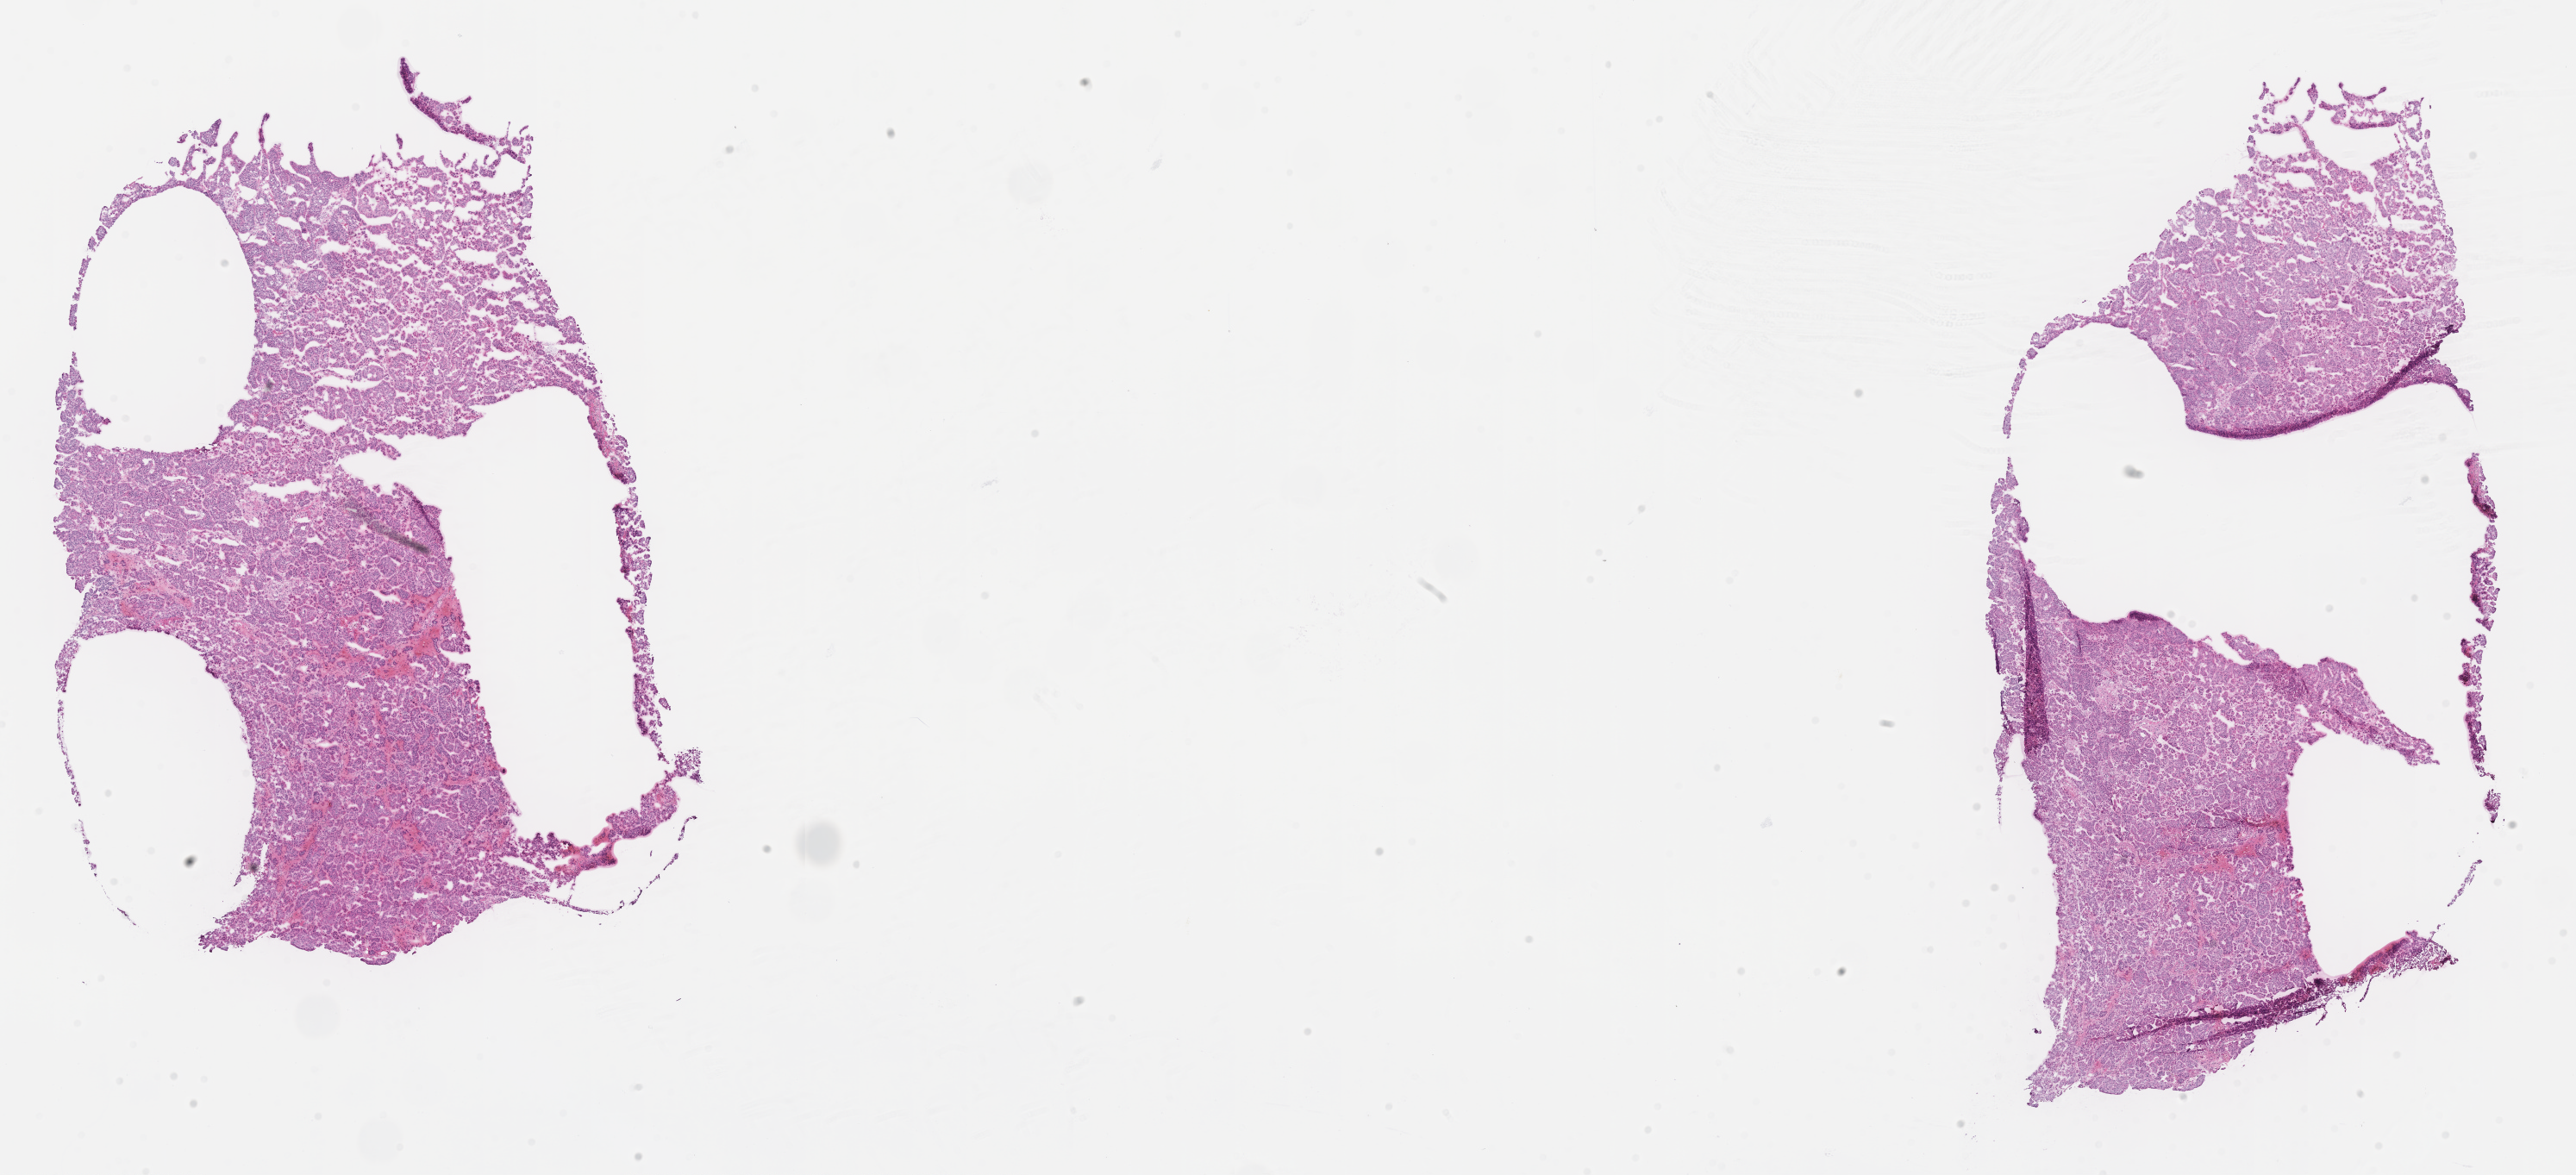
Digitized haematoxylin and eosin-stained section, whole scanned area (about 24.1 x 11.0 mm) shown as a low-resolution overview, frozen section, specimen: primary tumor, anatomic site: breast (left). Female patient; age at initial diagnosis 69 years. Slide review estimates, as recorded: tumor cells 90%, tumor nuclei 90%, stromal cells 10%, necrosis 0%, normal cells 0%. Infiltration values recorded for this section: lymphocyte infiltration 4%, monocyte infiltration 1%, neutrophil infiltration 2%.
Diagnosis: Infiltrating duct carcinoma, NOS.